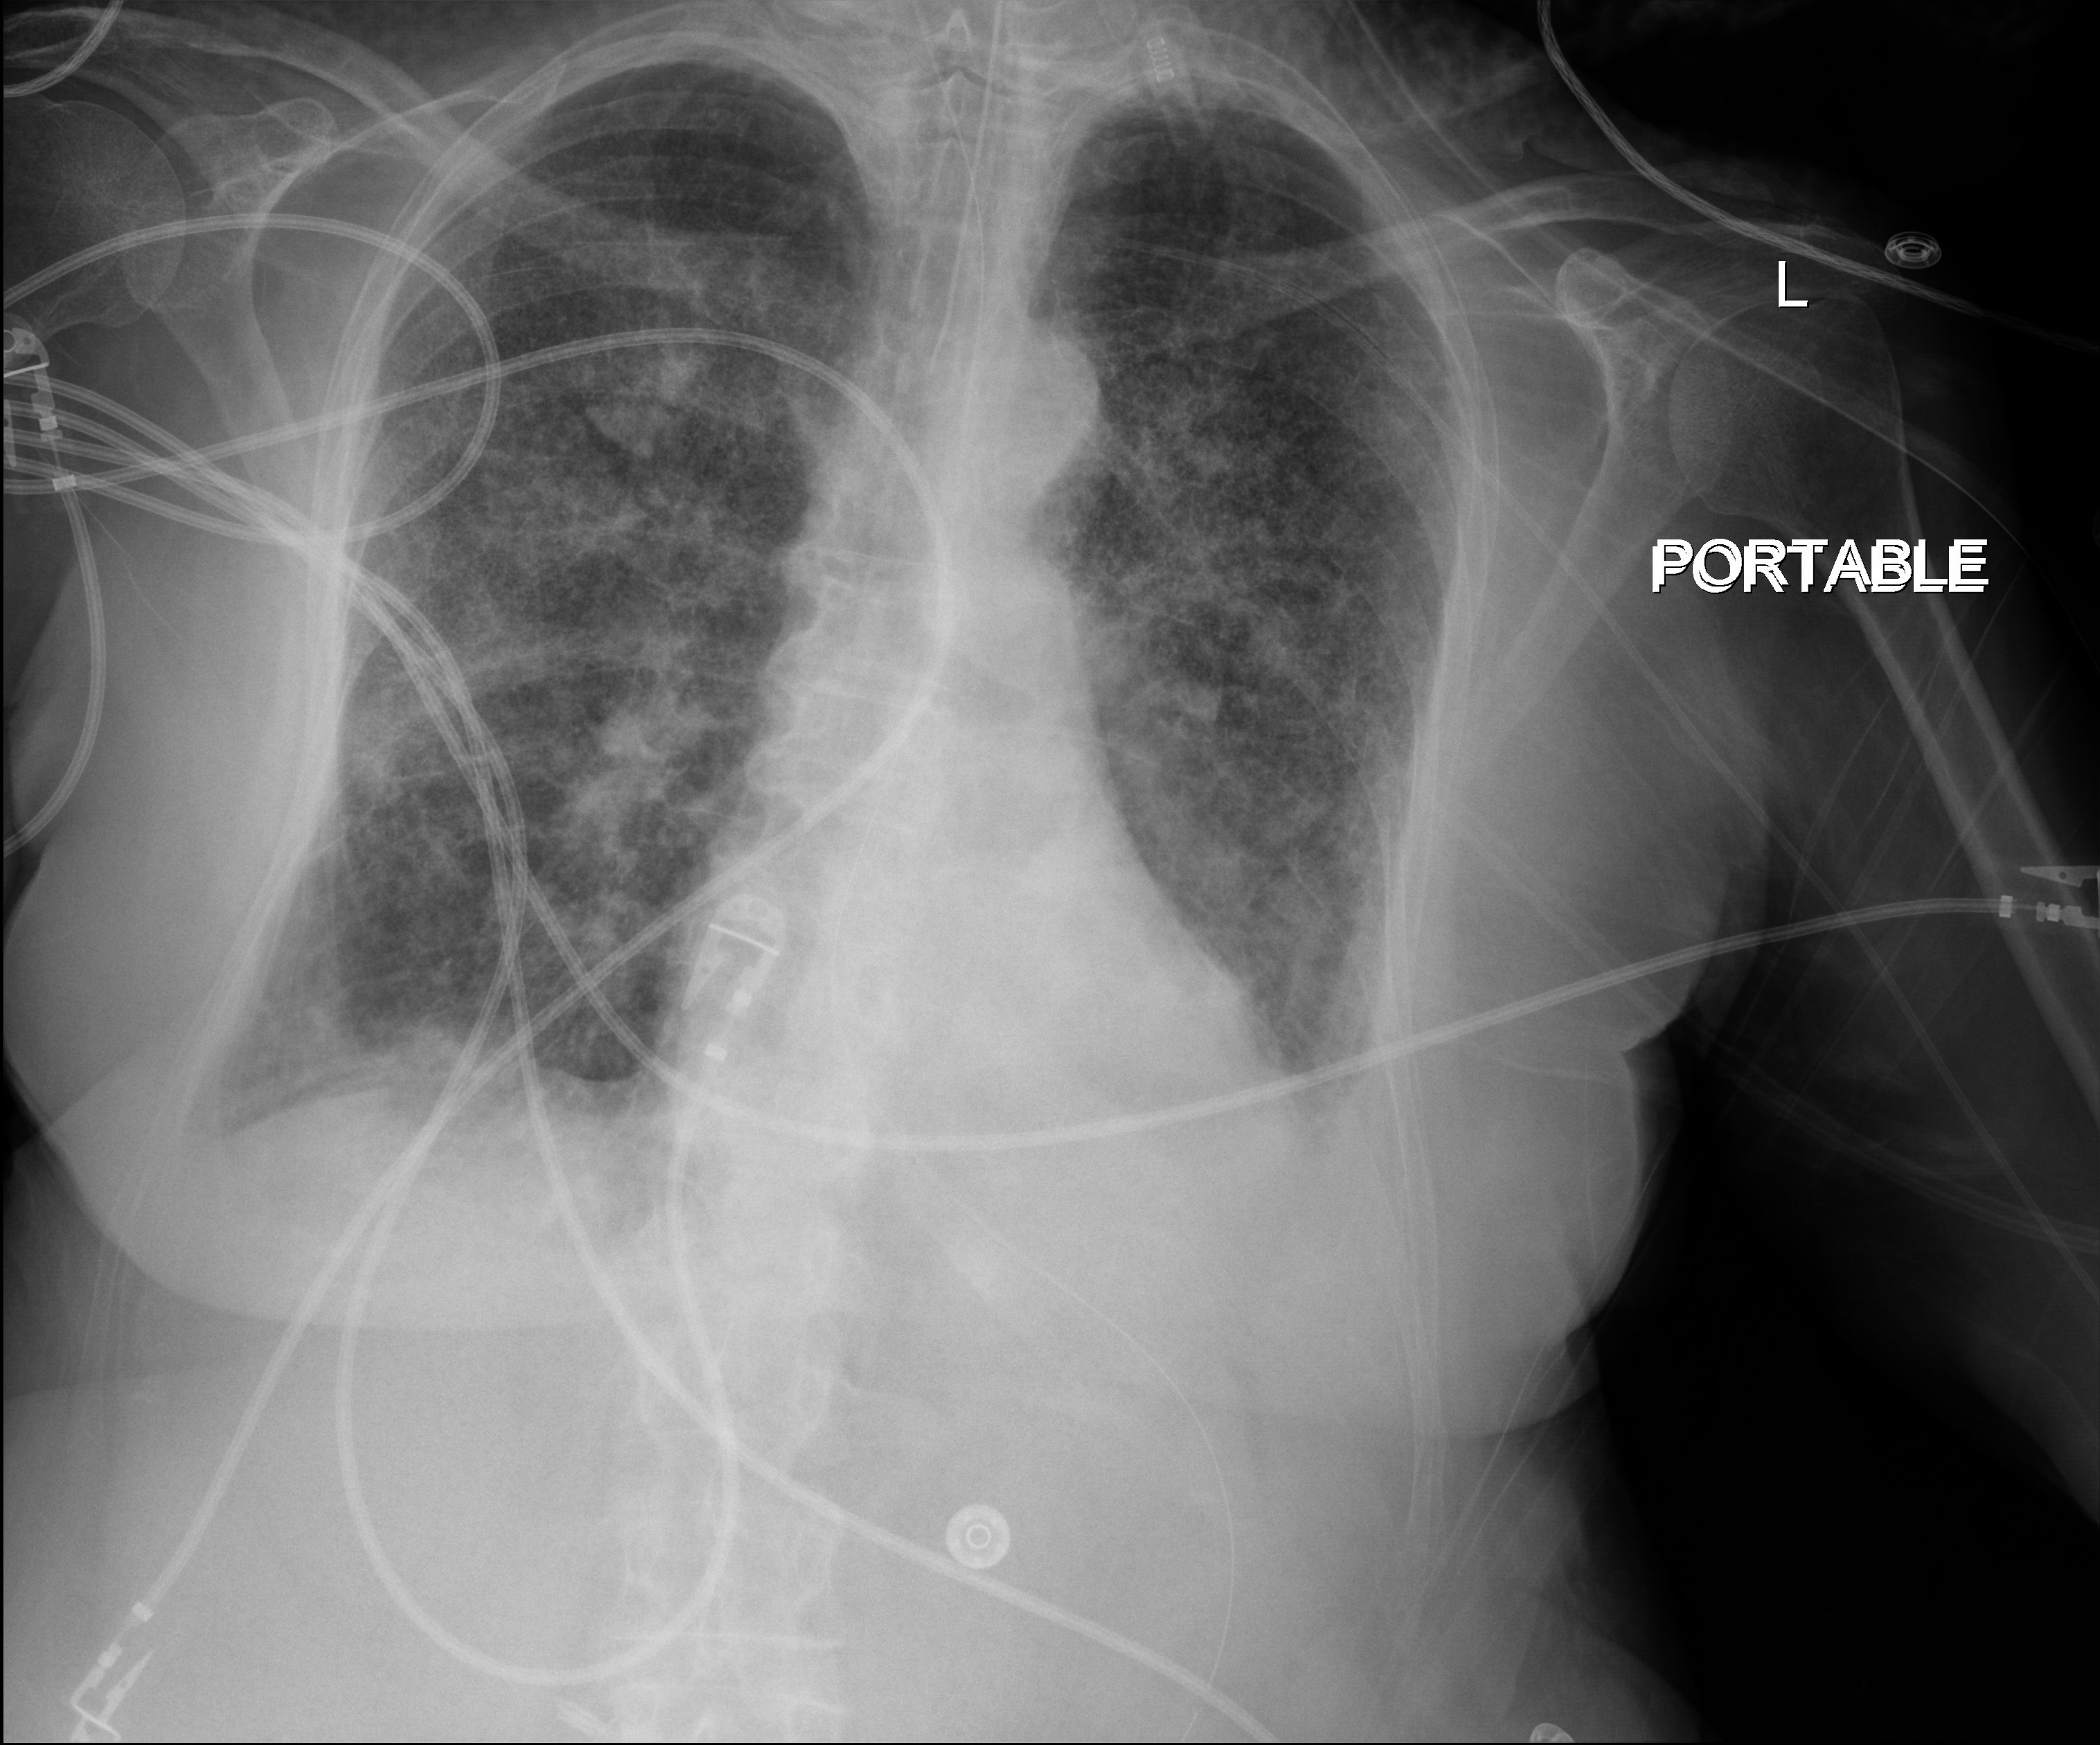
Chest X-ray (portable); anteroposterior (AP) projection. Female patient hospitalised with COVID-19, age 75–90 years.
From the hospital-stay record, not from the radiograph (when in the stay this image was taken is not recorded):
- mechanically ventilated during this hospital stay: yes
- chronic kidney disease (admission record): no
- length of hospital stay: 70 days